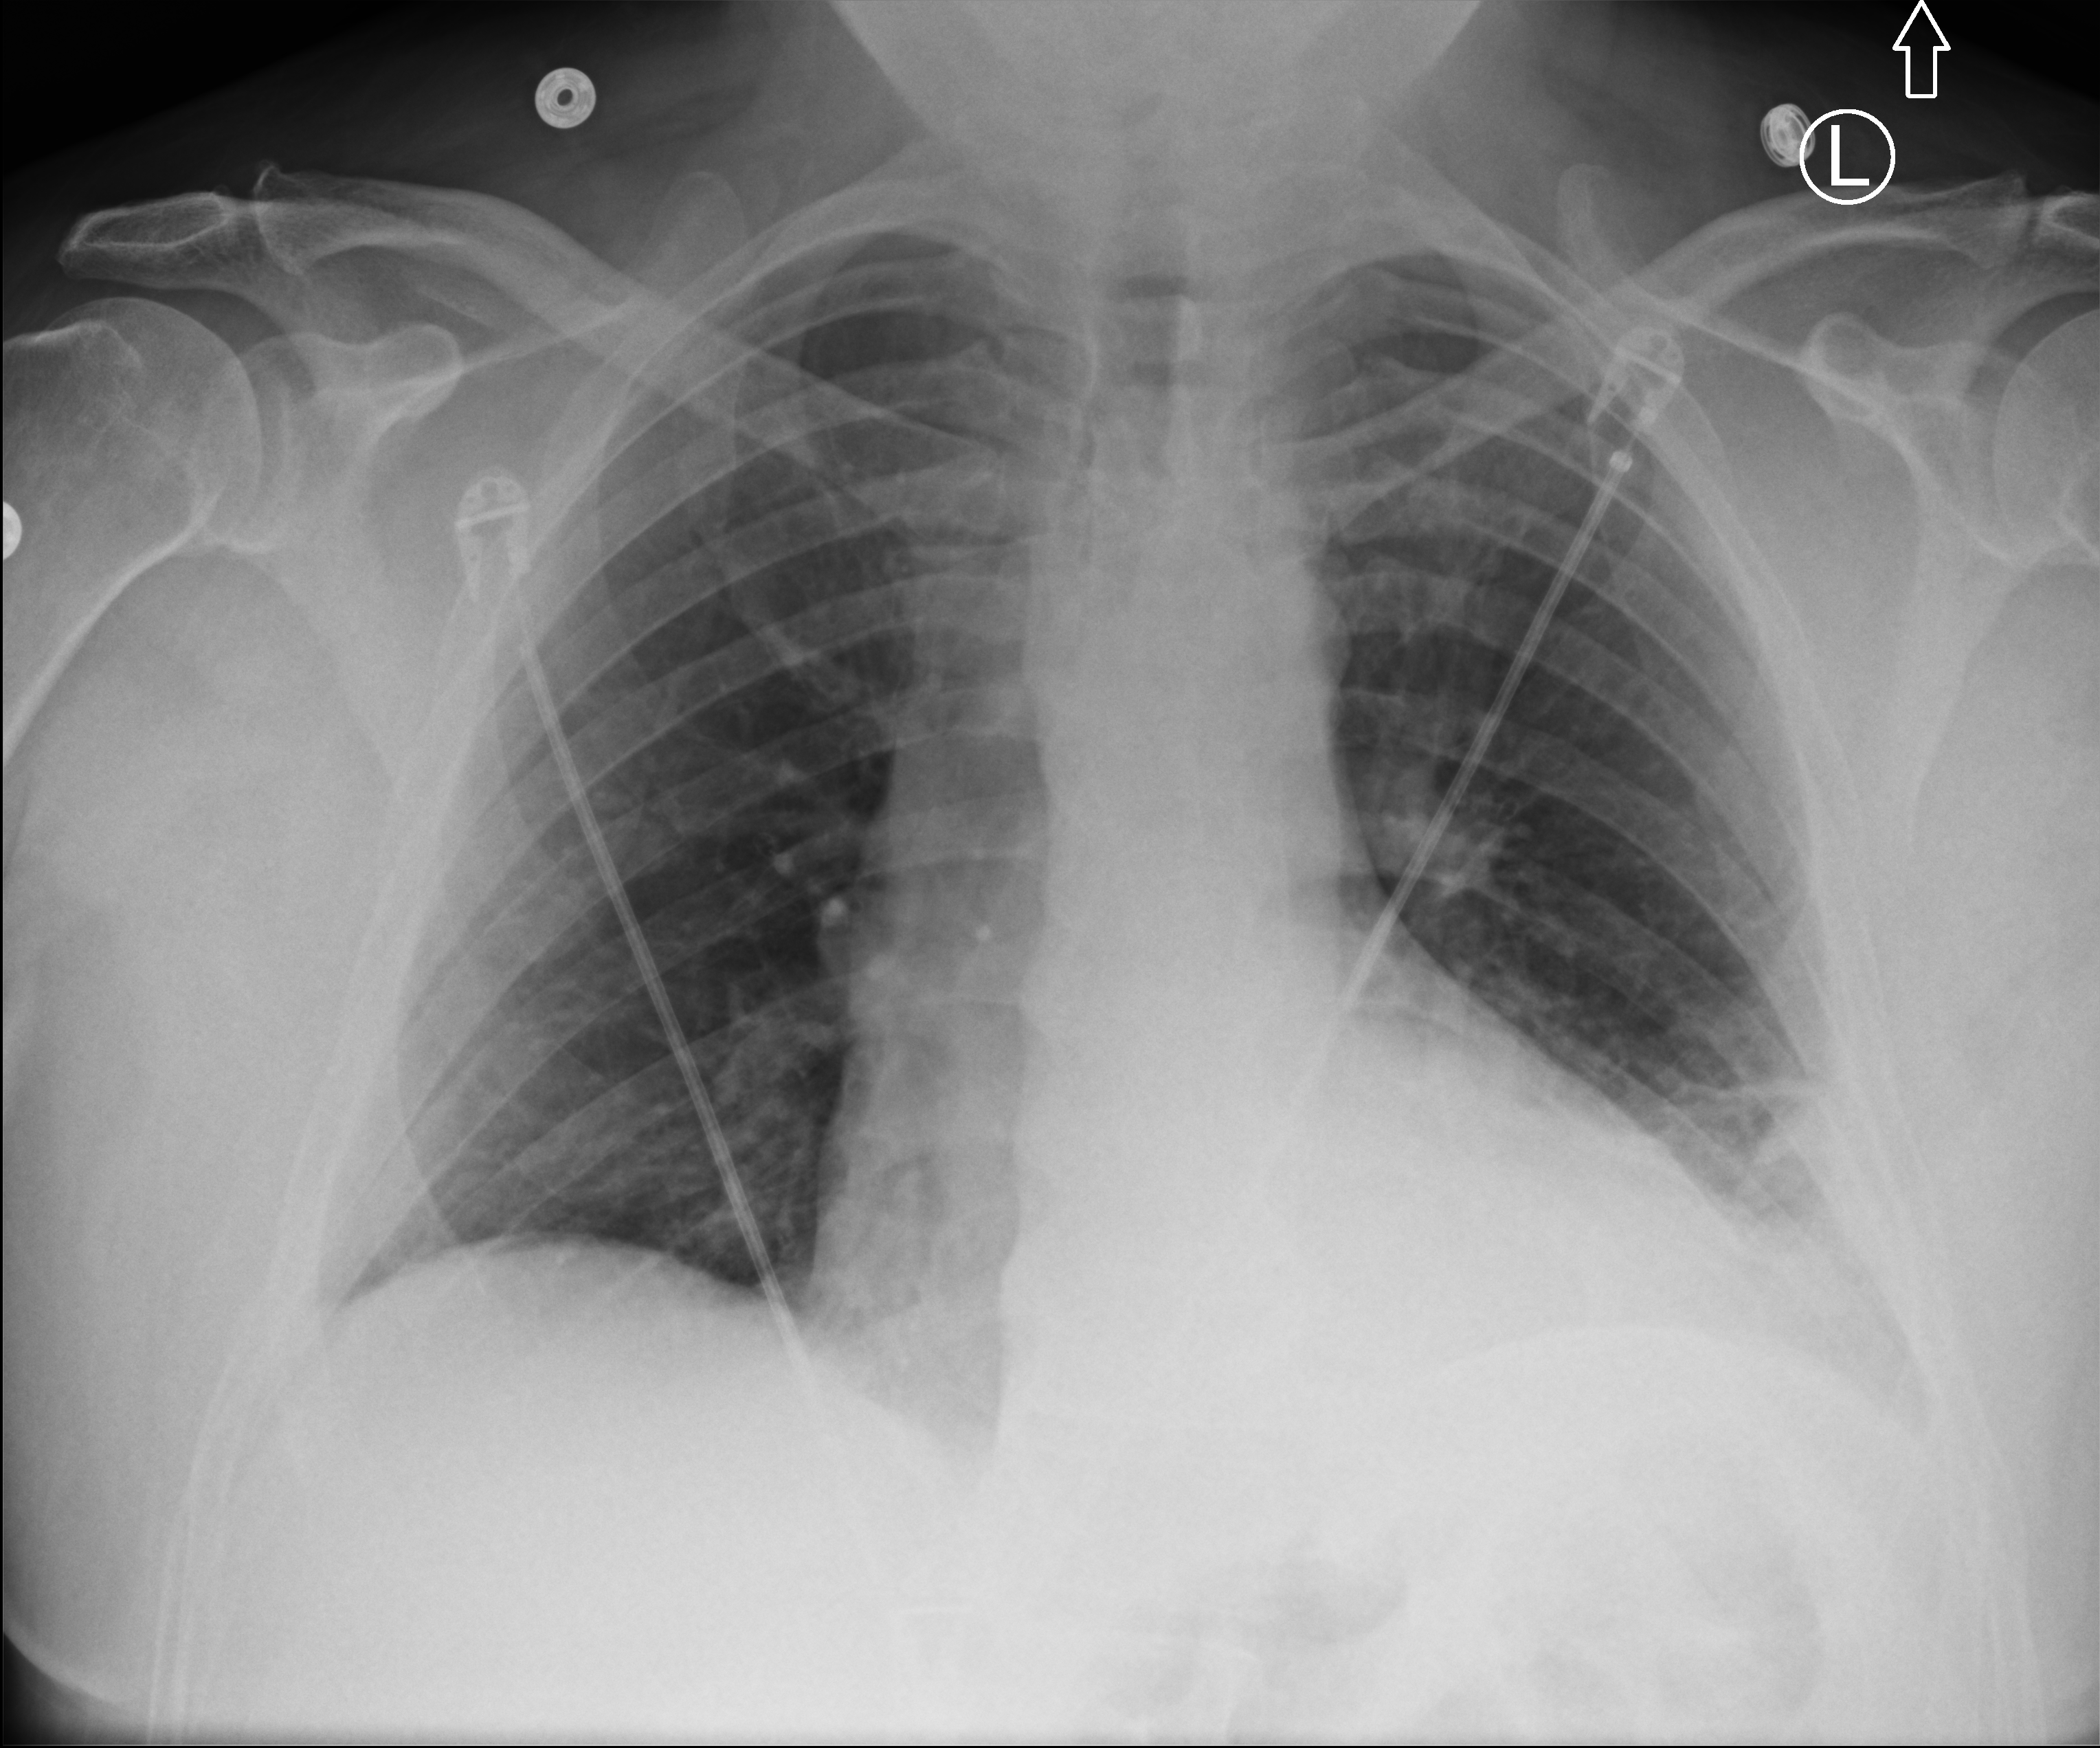
Portable chest radiograph, anteroposterior (AP) projection. Male patient hospitalised with COVID-19, age 18–59 years.
From the hospital-stay record, not from the radiograph (when in the stay this image was taken is not recorded):
- admitted to intensive care during this hospital stay: no
- mechanically ventilated during this hospital stay: no
- length of hospital stay: 10 days